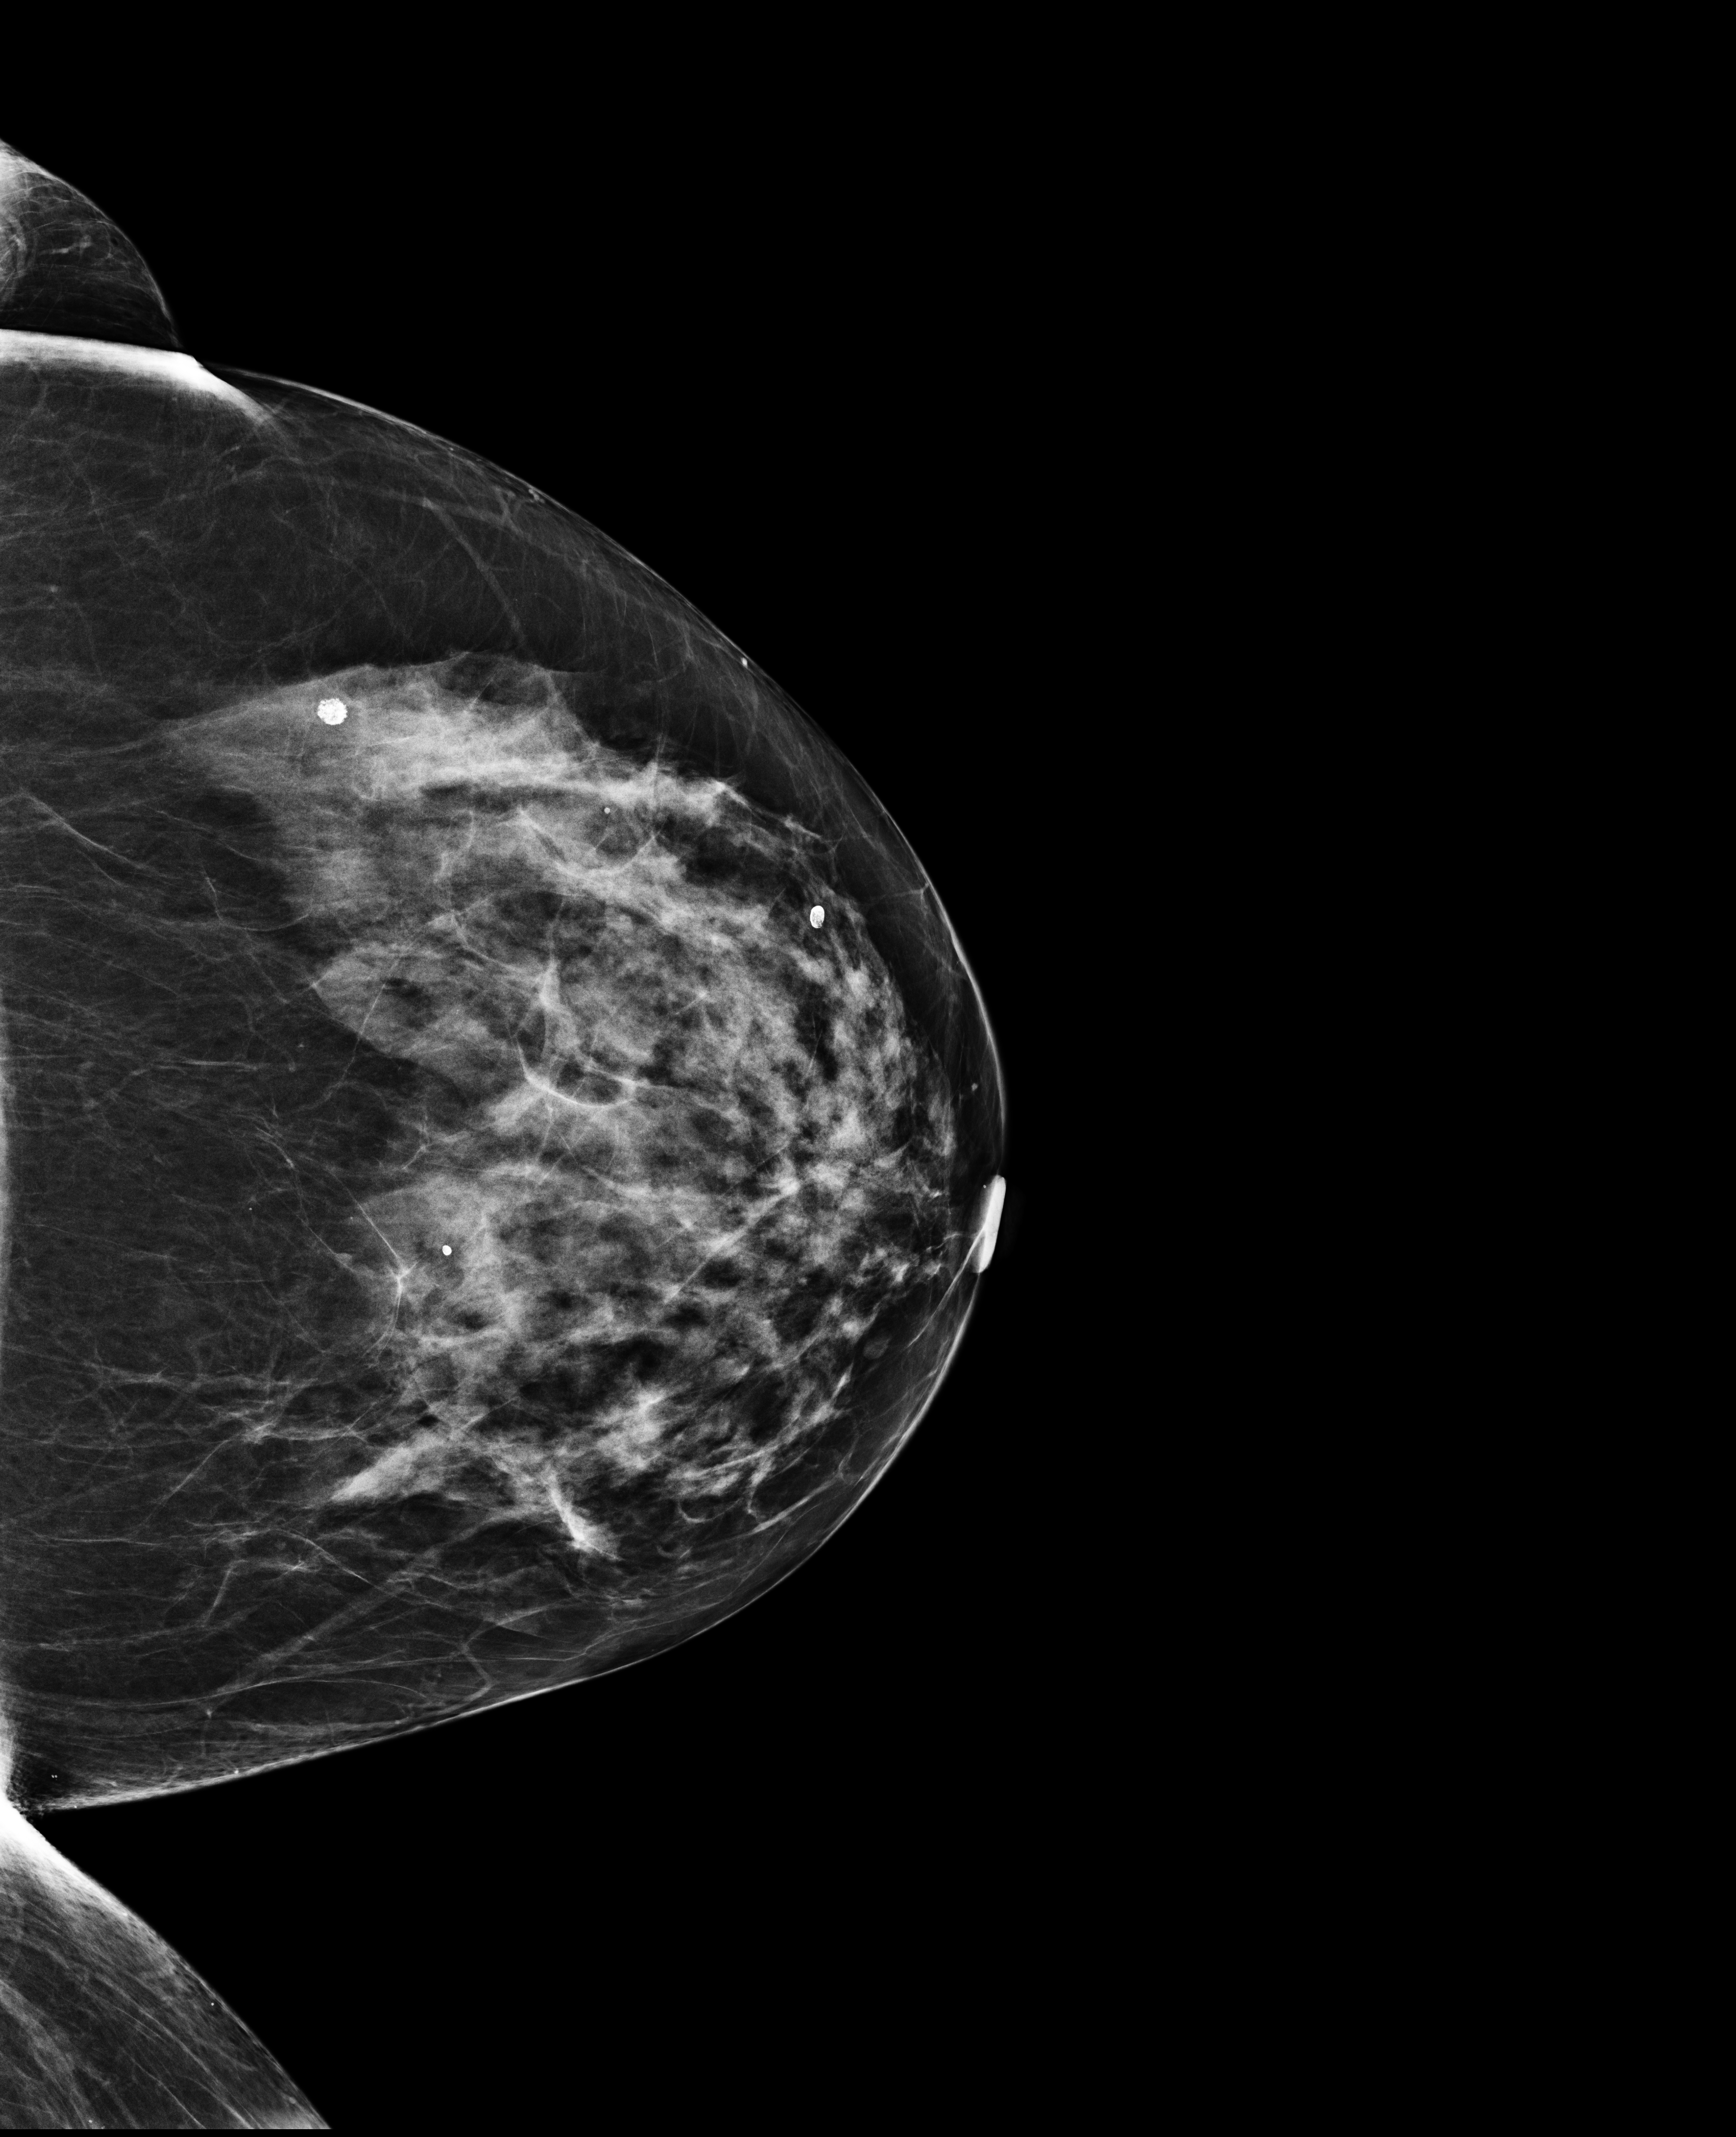
Screening examination; system: Selenia Dimensions. Patient aged 63 years (female).
Image type: full-field digital mammogram. Breast: left. Projection: CC view.